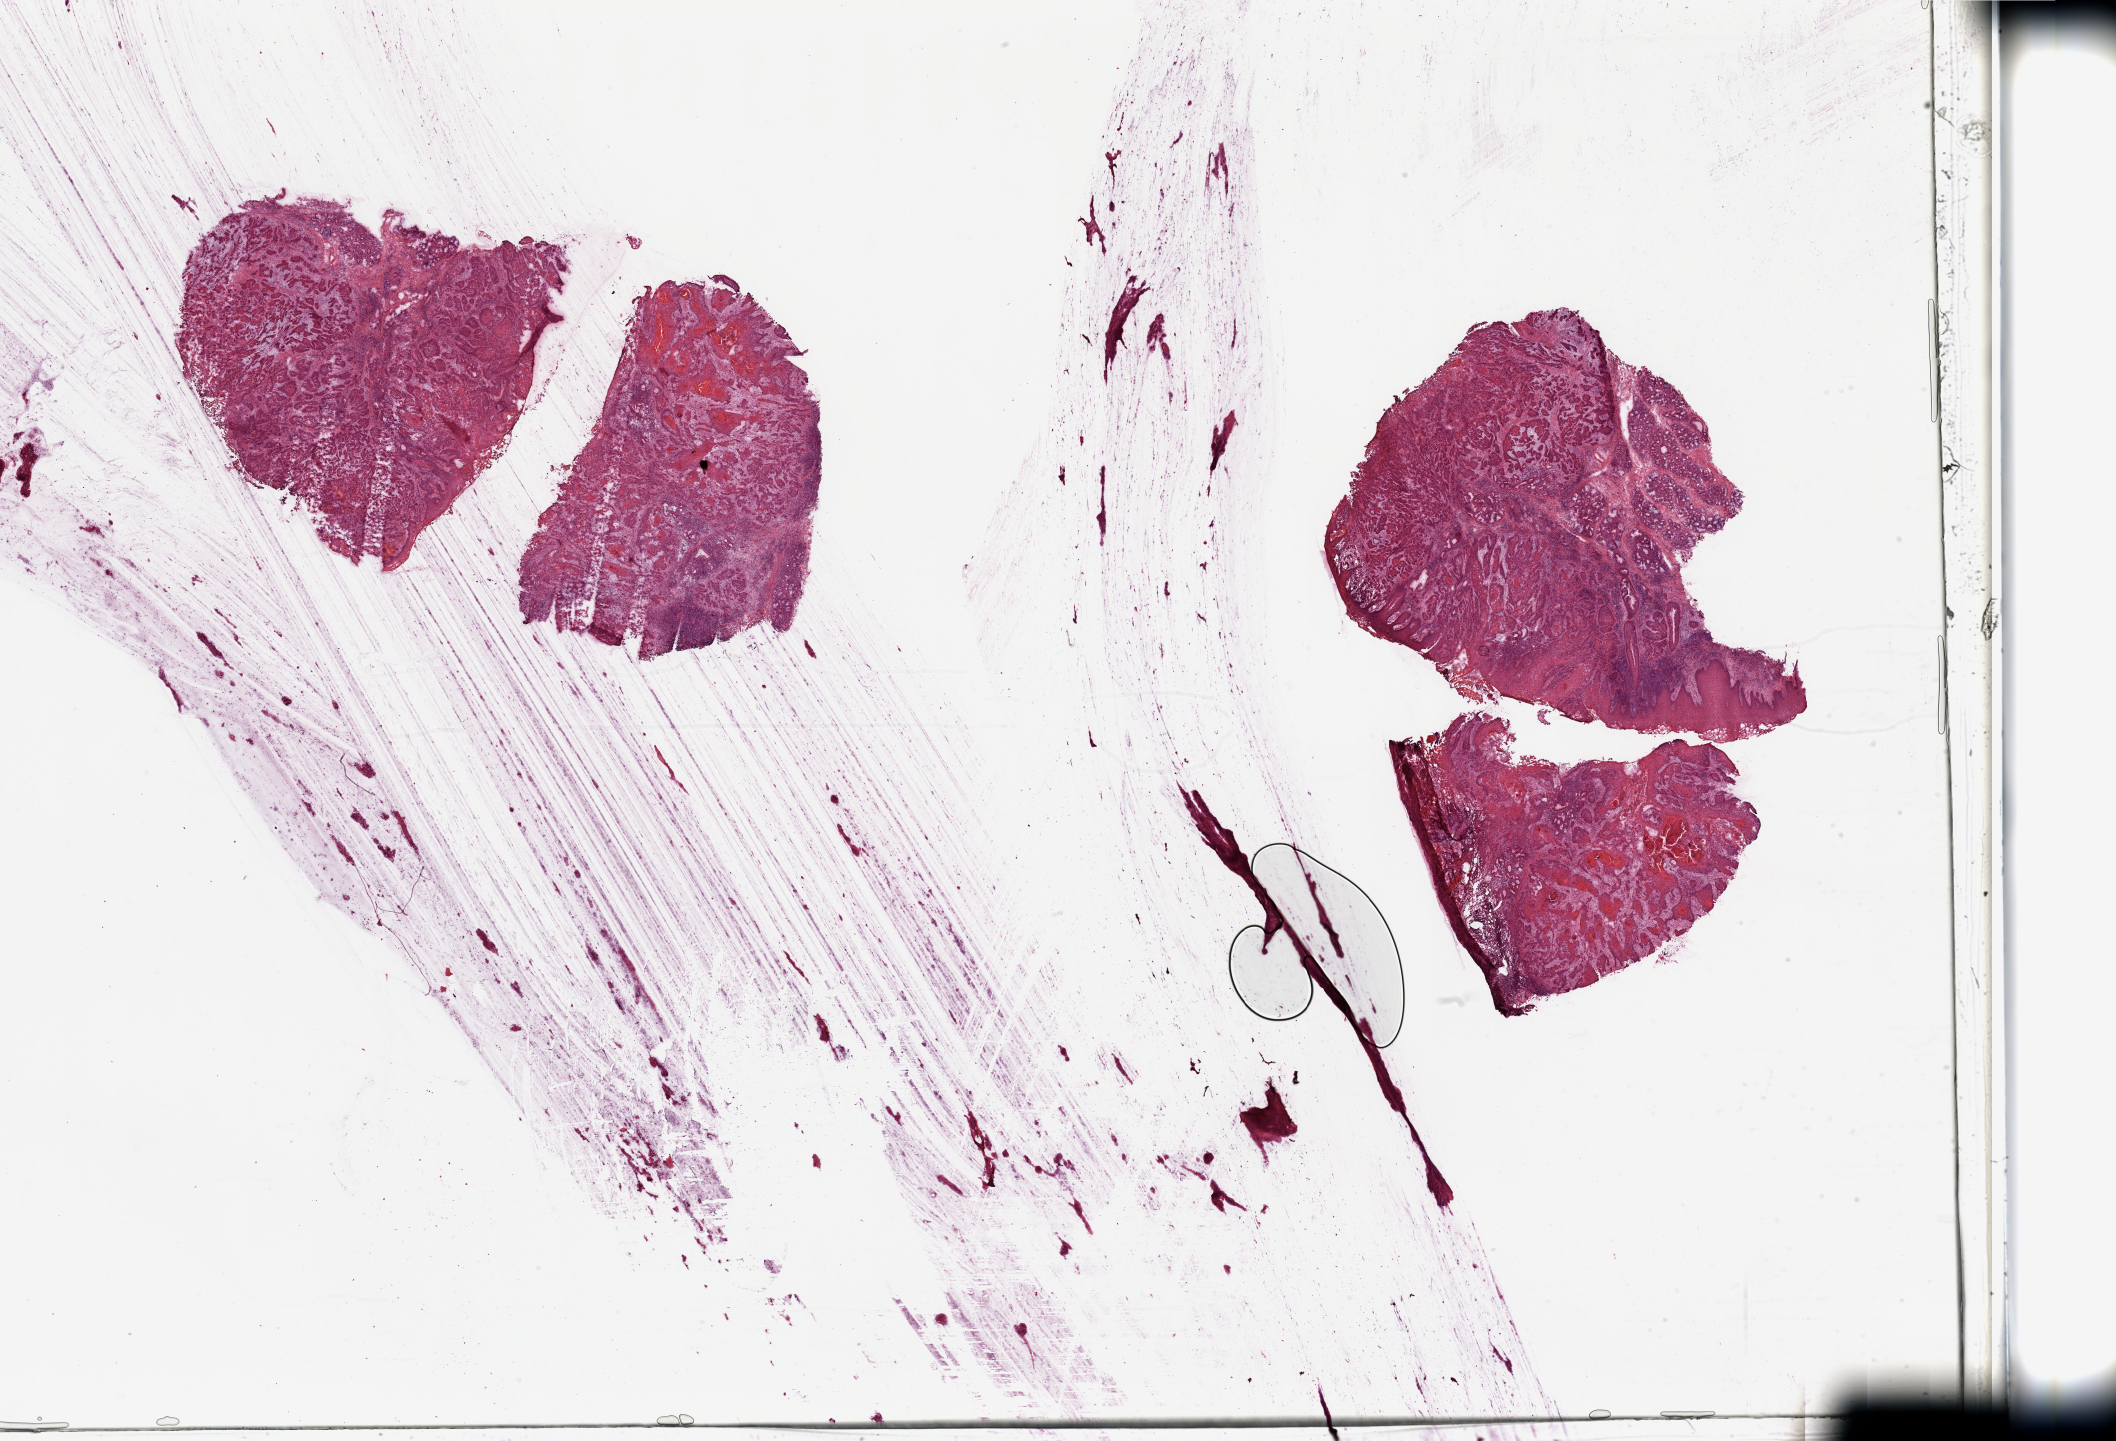
Whole-slide histology image, Hematoxylin and eosin (H&E) stained, low-resolution overview of the scanned area, about 33.5 x 22.8 mm (acquisition: 20x scan). Tumour tissue sample, sampled site: larynx. 54-year-old female patient. Histologic grade: G2 (moderately differentiated). Slide review estimates, as recorded: tumour nuclei 80%, necrosis 5%.
AJCC pathologic stage: III. Diagnosis: Squamous cell carcinoma, NOS (larynx, NOS).